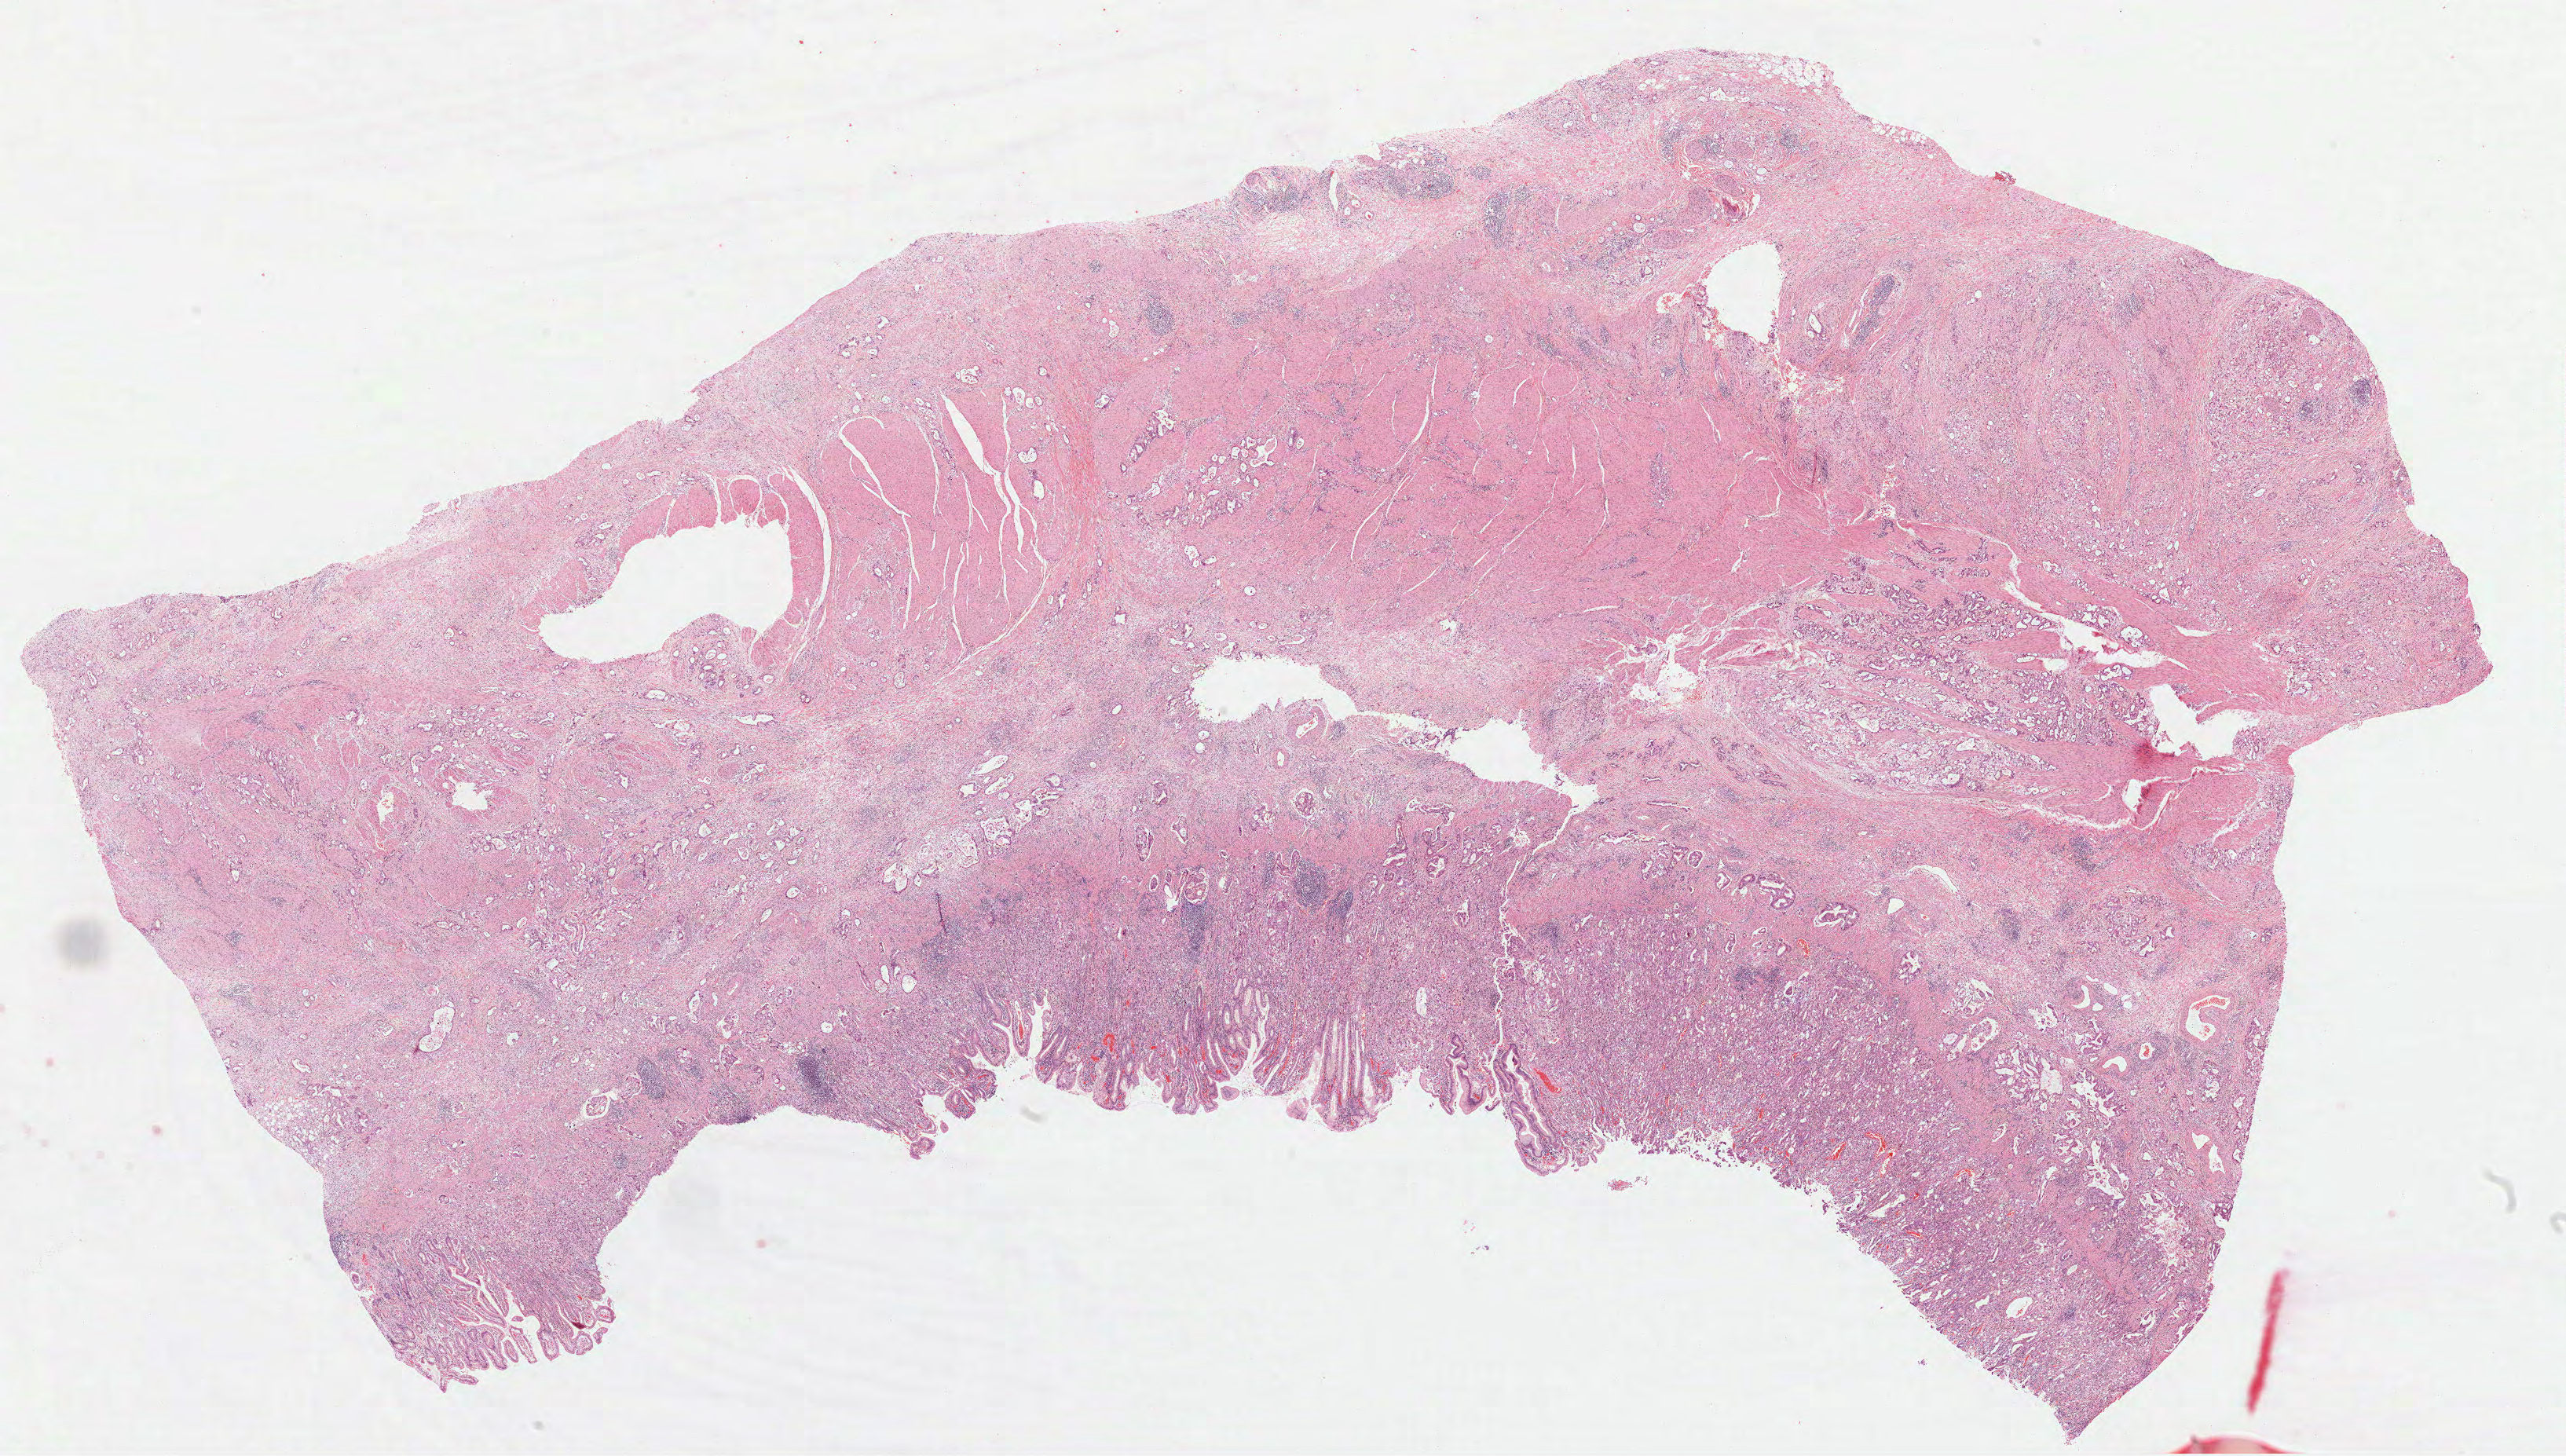
H&E whole-slide image, a low-resolution overview of the entire scanned area, about 26.3 x 15.0 mm; formalin-fixed paraffin-embedded (FFPE) diagnostic section; sample: primary tumour, stomach. Male patient; age at initial diagnosis 62 years.
Diagnosis: Adenocarcinoma, NOS (fundus of stomach).